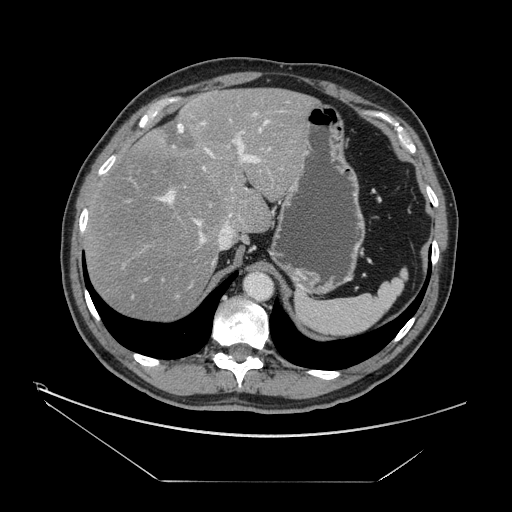
Contrast-enhanced abdominal CT, one axial slice. Reconstruction kernel STANDARD. 120 kVp. Intravenous contrast given. Soft-tissue window (W 400 / L 40 HU). 2.5 mm slice thickness. 512 × 512 image matrix, field of view 440 × 440 mm. Male patient, age 65 years. Case-level facts recorded for this patient, not image findings: diagnosis: colorectal cancer liver metastases, imaged before liver resection; multiple liver metastases: yes; largest metastasis: 4.2 cm; chemotherapy before resection: yes.
Annotated regions visible in this slice (outlined manually by an expert reader):
- hepatic veins: bounding box (x1, y1, x2, y2) in pixels: (197, 121, 268, 265)
- liver: (85, 89, 314, 321)
- planned liver remnant (the part of the liver to remain after resection): (85, 89, 314, 321)
- portal vein (with intrahepatic branches): (156, 110, 284, 225)
- liver metastasis: (164, 122, 196, 153)